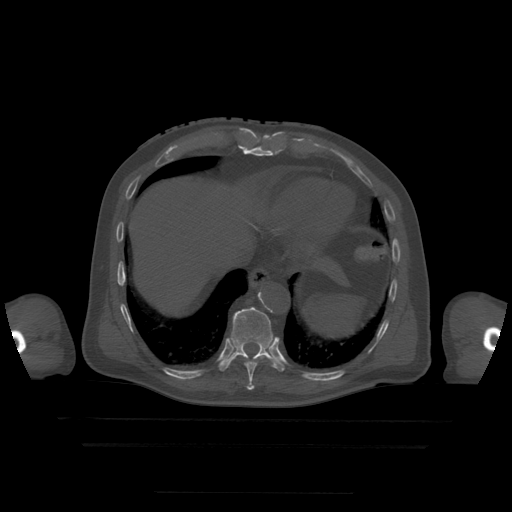
CT including the spine, one axial slice. Position 249 of 522 along the scan axis. Bone window (W 1800 / L 400 HU). 1.25 mm slice thickness. 512 × 512 image matrix, field of view 436 × 436 mm. Patient age 68 years. From the clinical record (not read from this slice): primary cancer: urothelial.
Outlined on this slice (semi-automatically segmented with operator editing):
- T10 vertebra: bounding box [x1, y1, x2, y2] px = [219, 307, 285, 372]
- T9 vertebra: [246, 357, 261, 391]